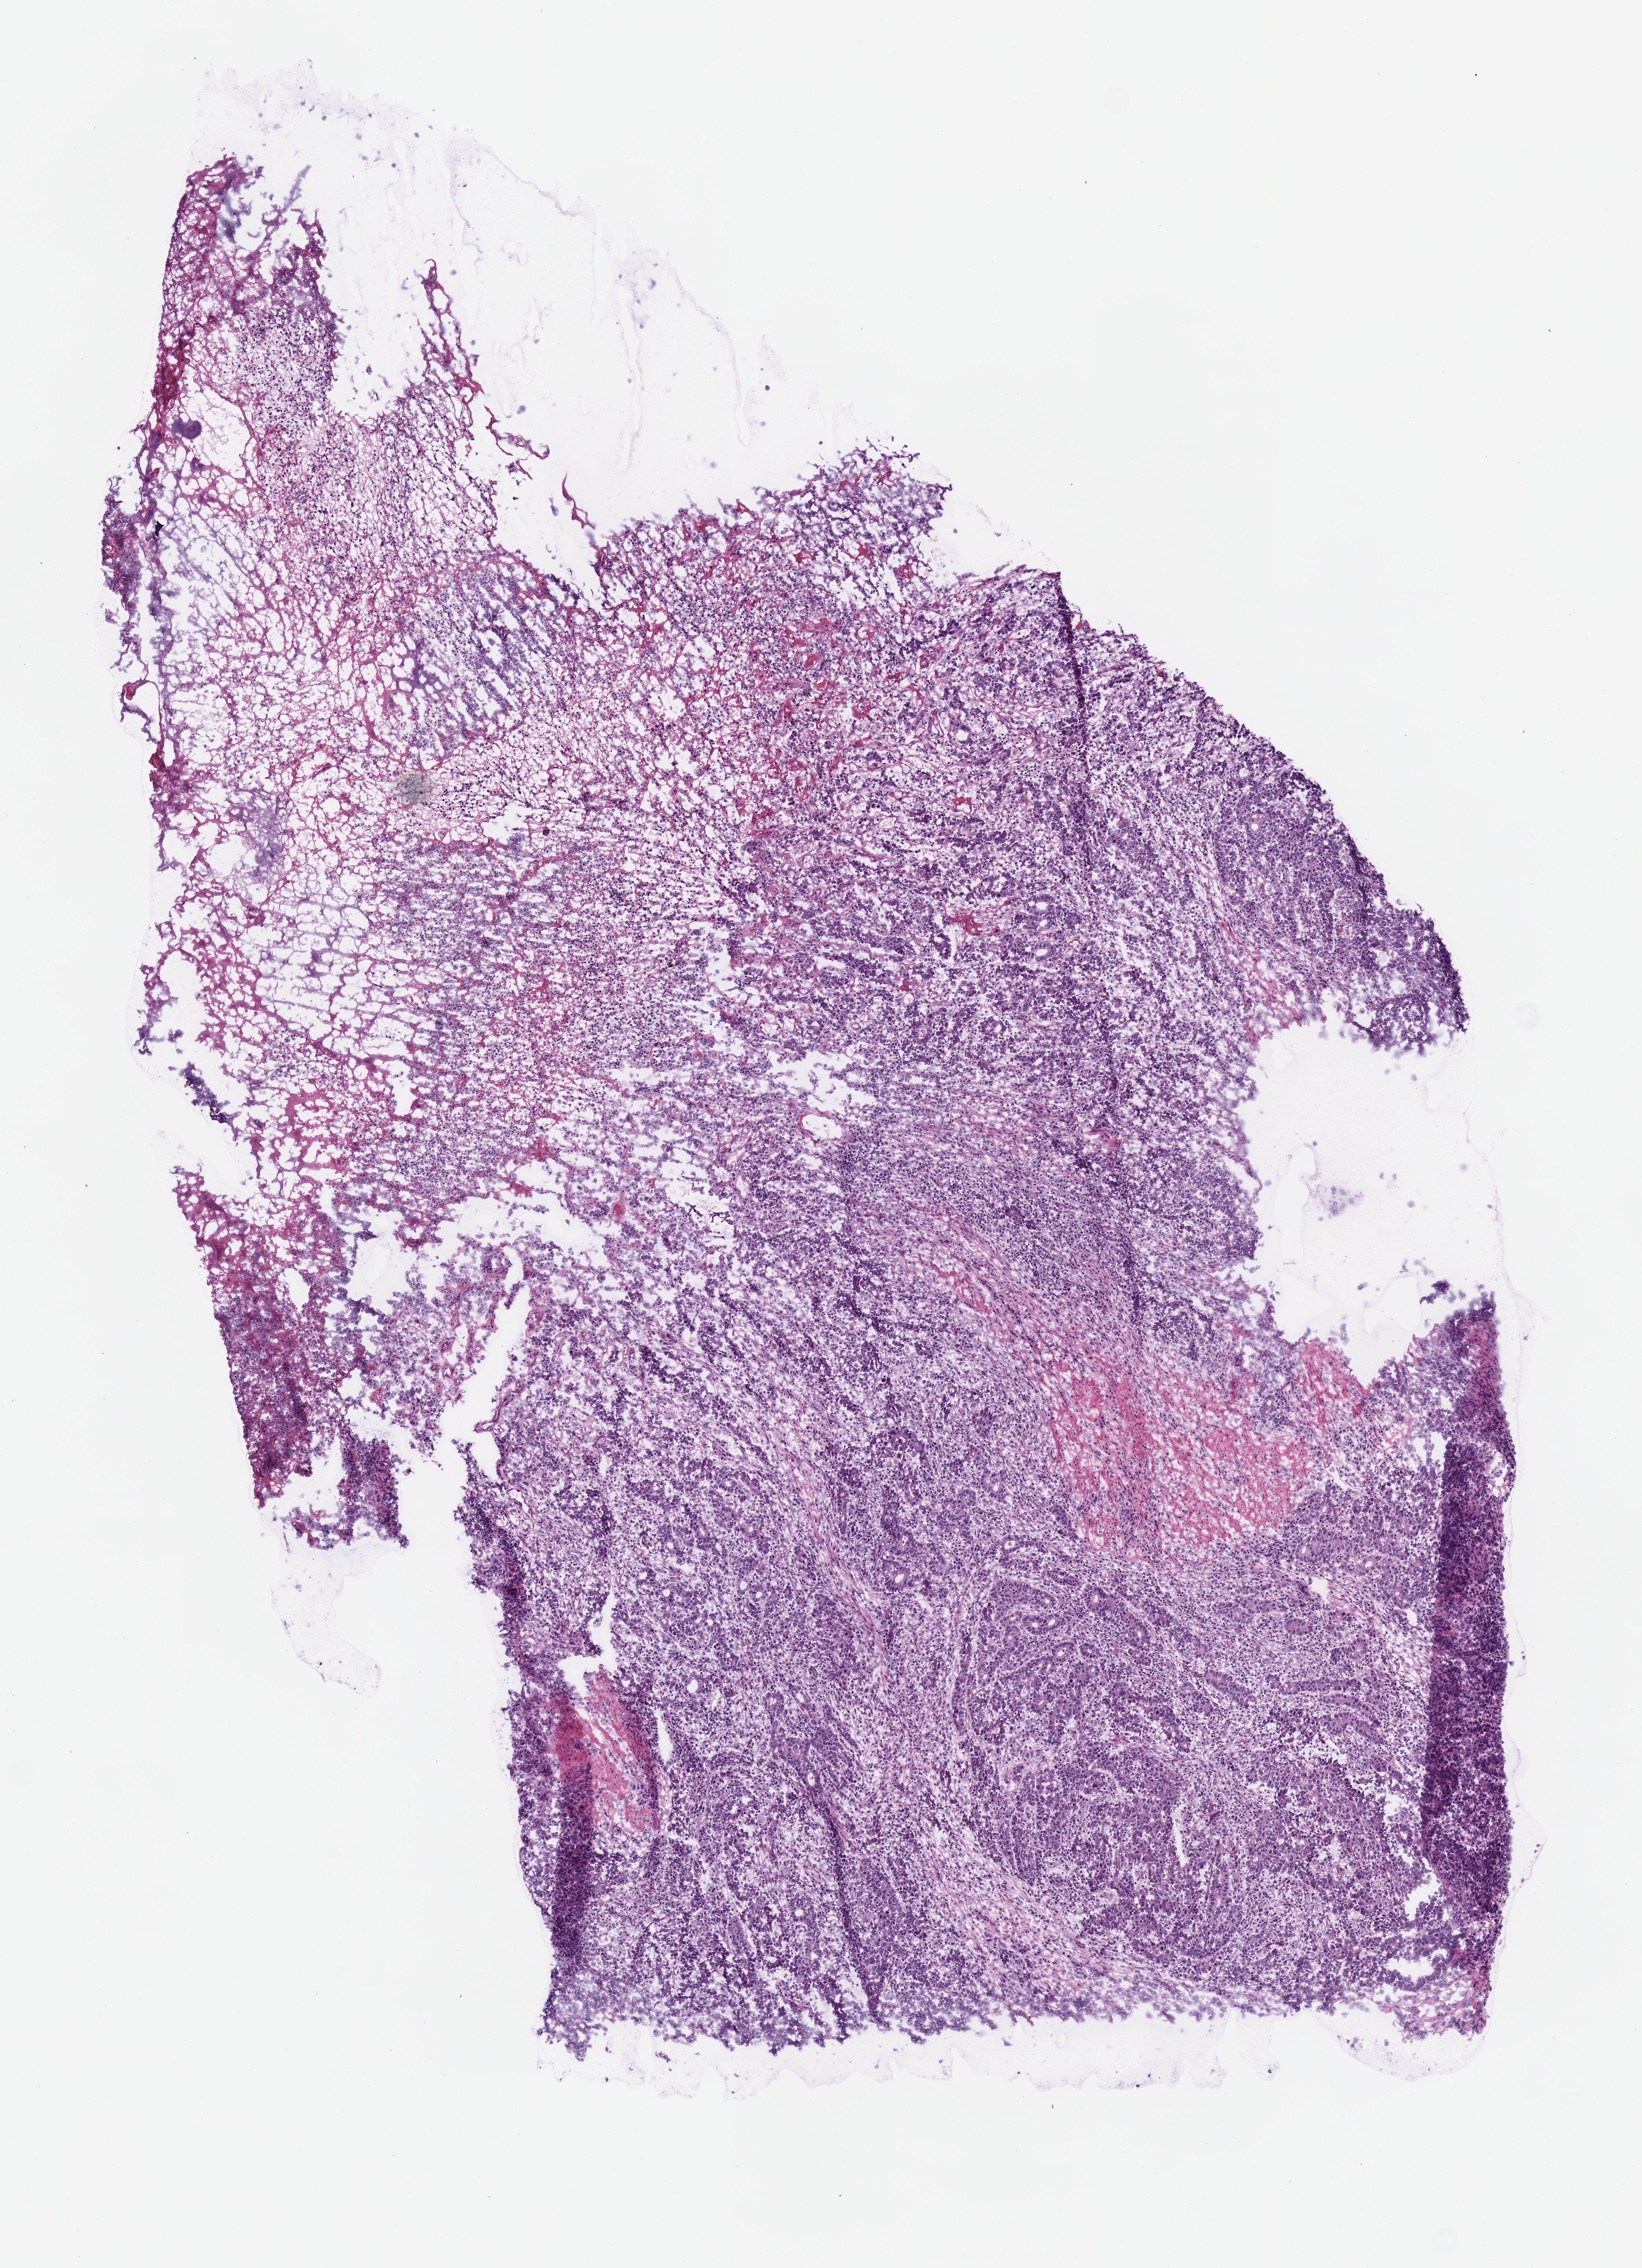
Digitized H&E-stained tissue section (whole slide) — whole scanned area (about 4.4 x 6.1 mm, slide scanned at 40x) shown as a low-resolution overview, frozen section from the top of the tissue portion, stomach, primary tumour sample. Female, age 82 years at initial diagnosis. Histologic grade: G2 (moderately differentiated). Slide review estimates, as recorded: tumour cells 75%, tumour nuclei 60%, normal cells 0%, stromal cells 25%, necrosis 0%.
* diagnosis: Tubular adenocarcinoma (gastric antrum)
* AJCC pathologic stage: IIA
* lymph nodes positive (case pathology): 0 of 27 examined